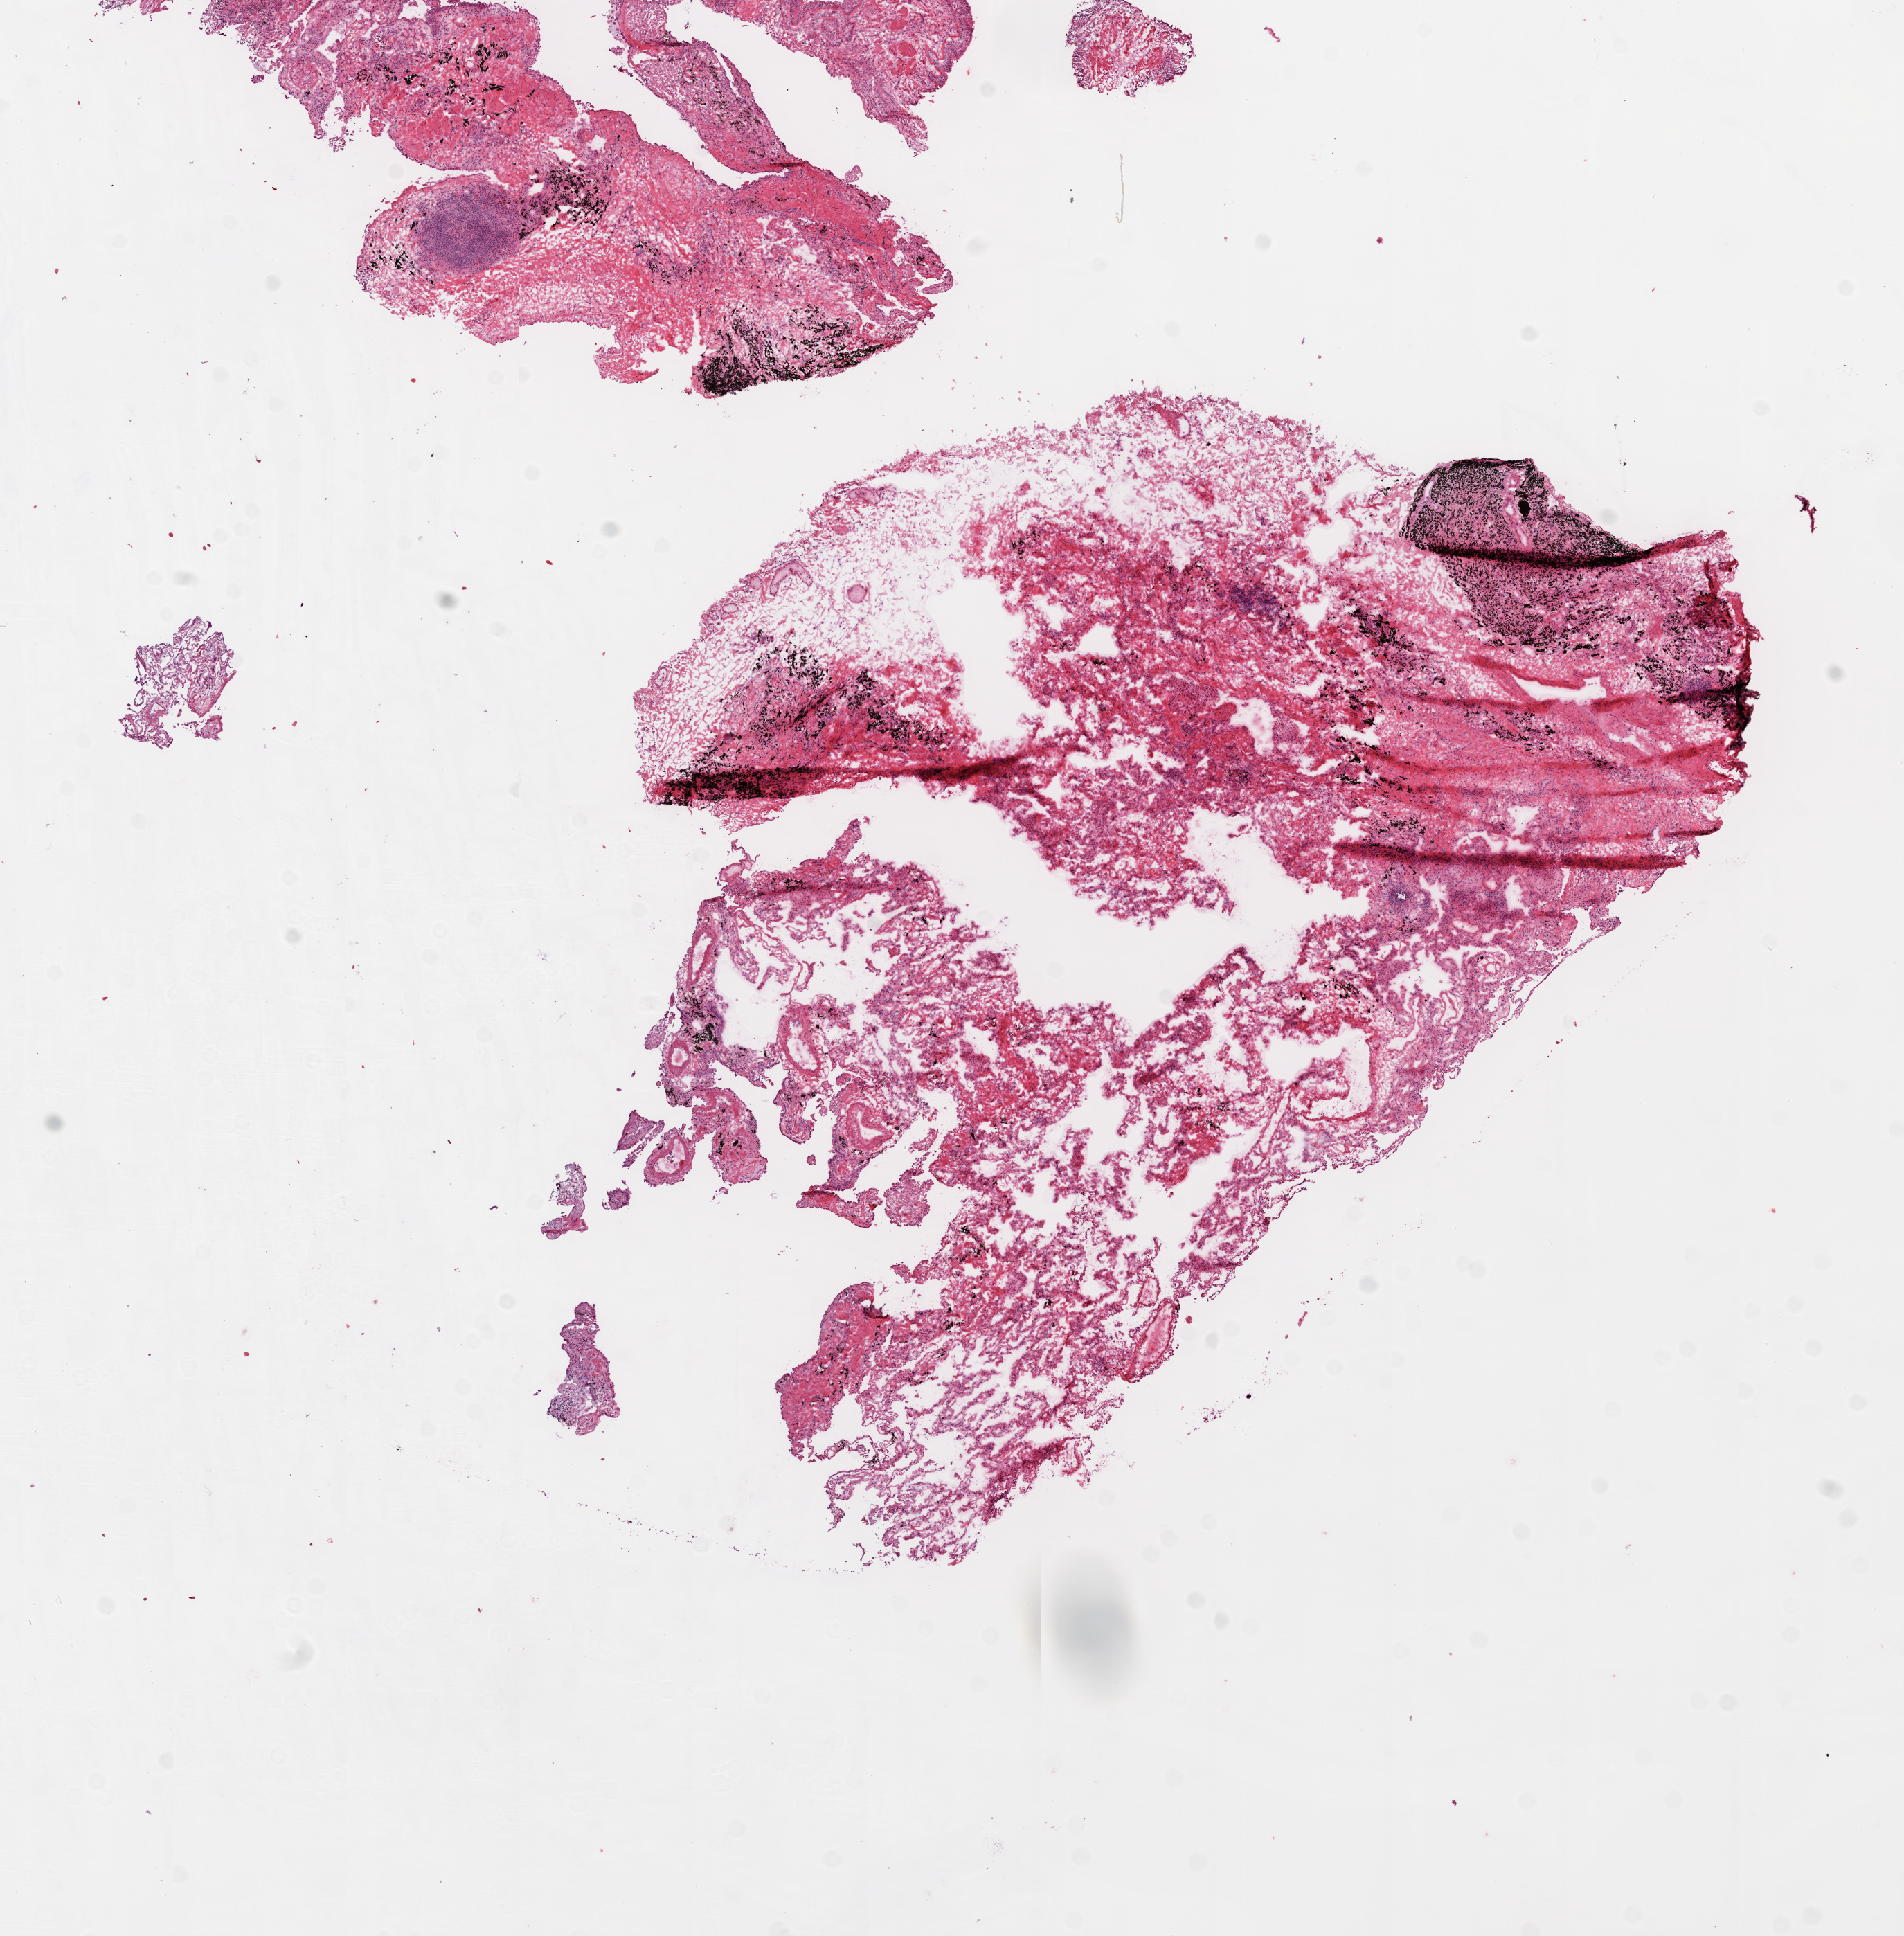
Whole-slide histology image, H&E-stained — shown as a low-resolution overview of the whole scanned area (about 11.0 x 11.2 mm, from a 20x scan); frozen section; lung, solid tissue normal (non-tumour tissue) sample. Male patient; age at initial diagnosis 75 years.
- this section: solid tissue normal (non-tumour) sample from the same patient
- patient diagnosis: Squamous cell carcinoma, NOS (lower lobe, lung)